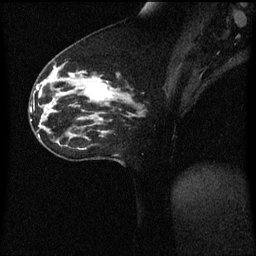
Breast MRI (dynamic contrast-enhanced), one sagittal slice; position 31 of 60 along the scan axis; dynamic contrast-enhanced series, image 2 of 3 at this slice position (ordered by acquisition); 1.5 T; TE 4.2 ms, TR 8.4 ms; 2 mm slice thickness; 256 × 256 image matrix, field of view 200 × 200 mm. Patient: female, 33 years. Case-level facts recorded for this patient, not image findings: setting: breast cancer imaged before/during neoadjuvant chemotherapy; receptor status: triple-negative.
Structures marked on this image (semi-automatically segmented with operator editing):
- analysis volume of interest (the breast-tissue region the enhancement analysis was run in; not a lesion): bounding box [x1, y1, x2, y2] px = [76, 70, 123, 113]
- tumour enhancement mask (voxels above the 70 % enhancement threshold inside the analysis volume of interest): [82, 78, 113, 101]